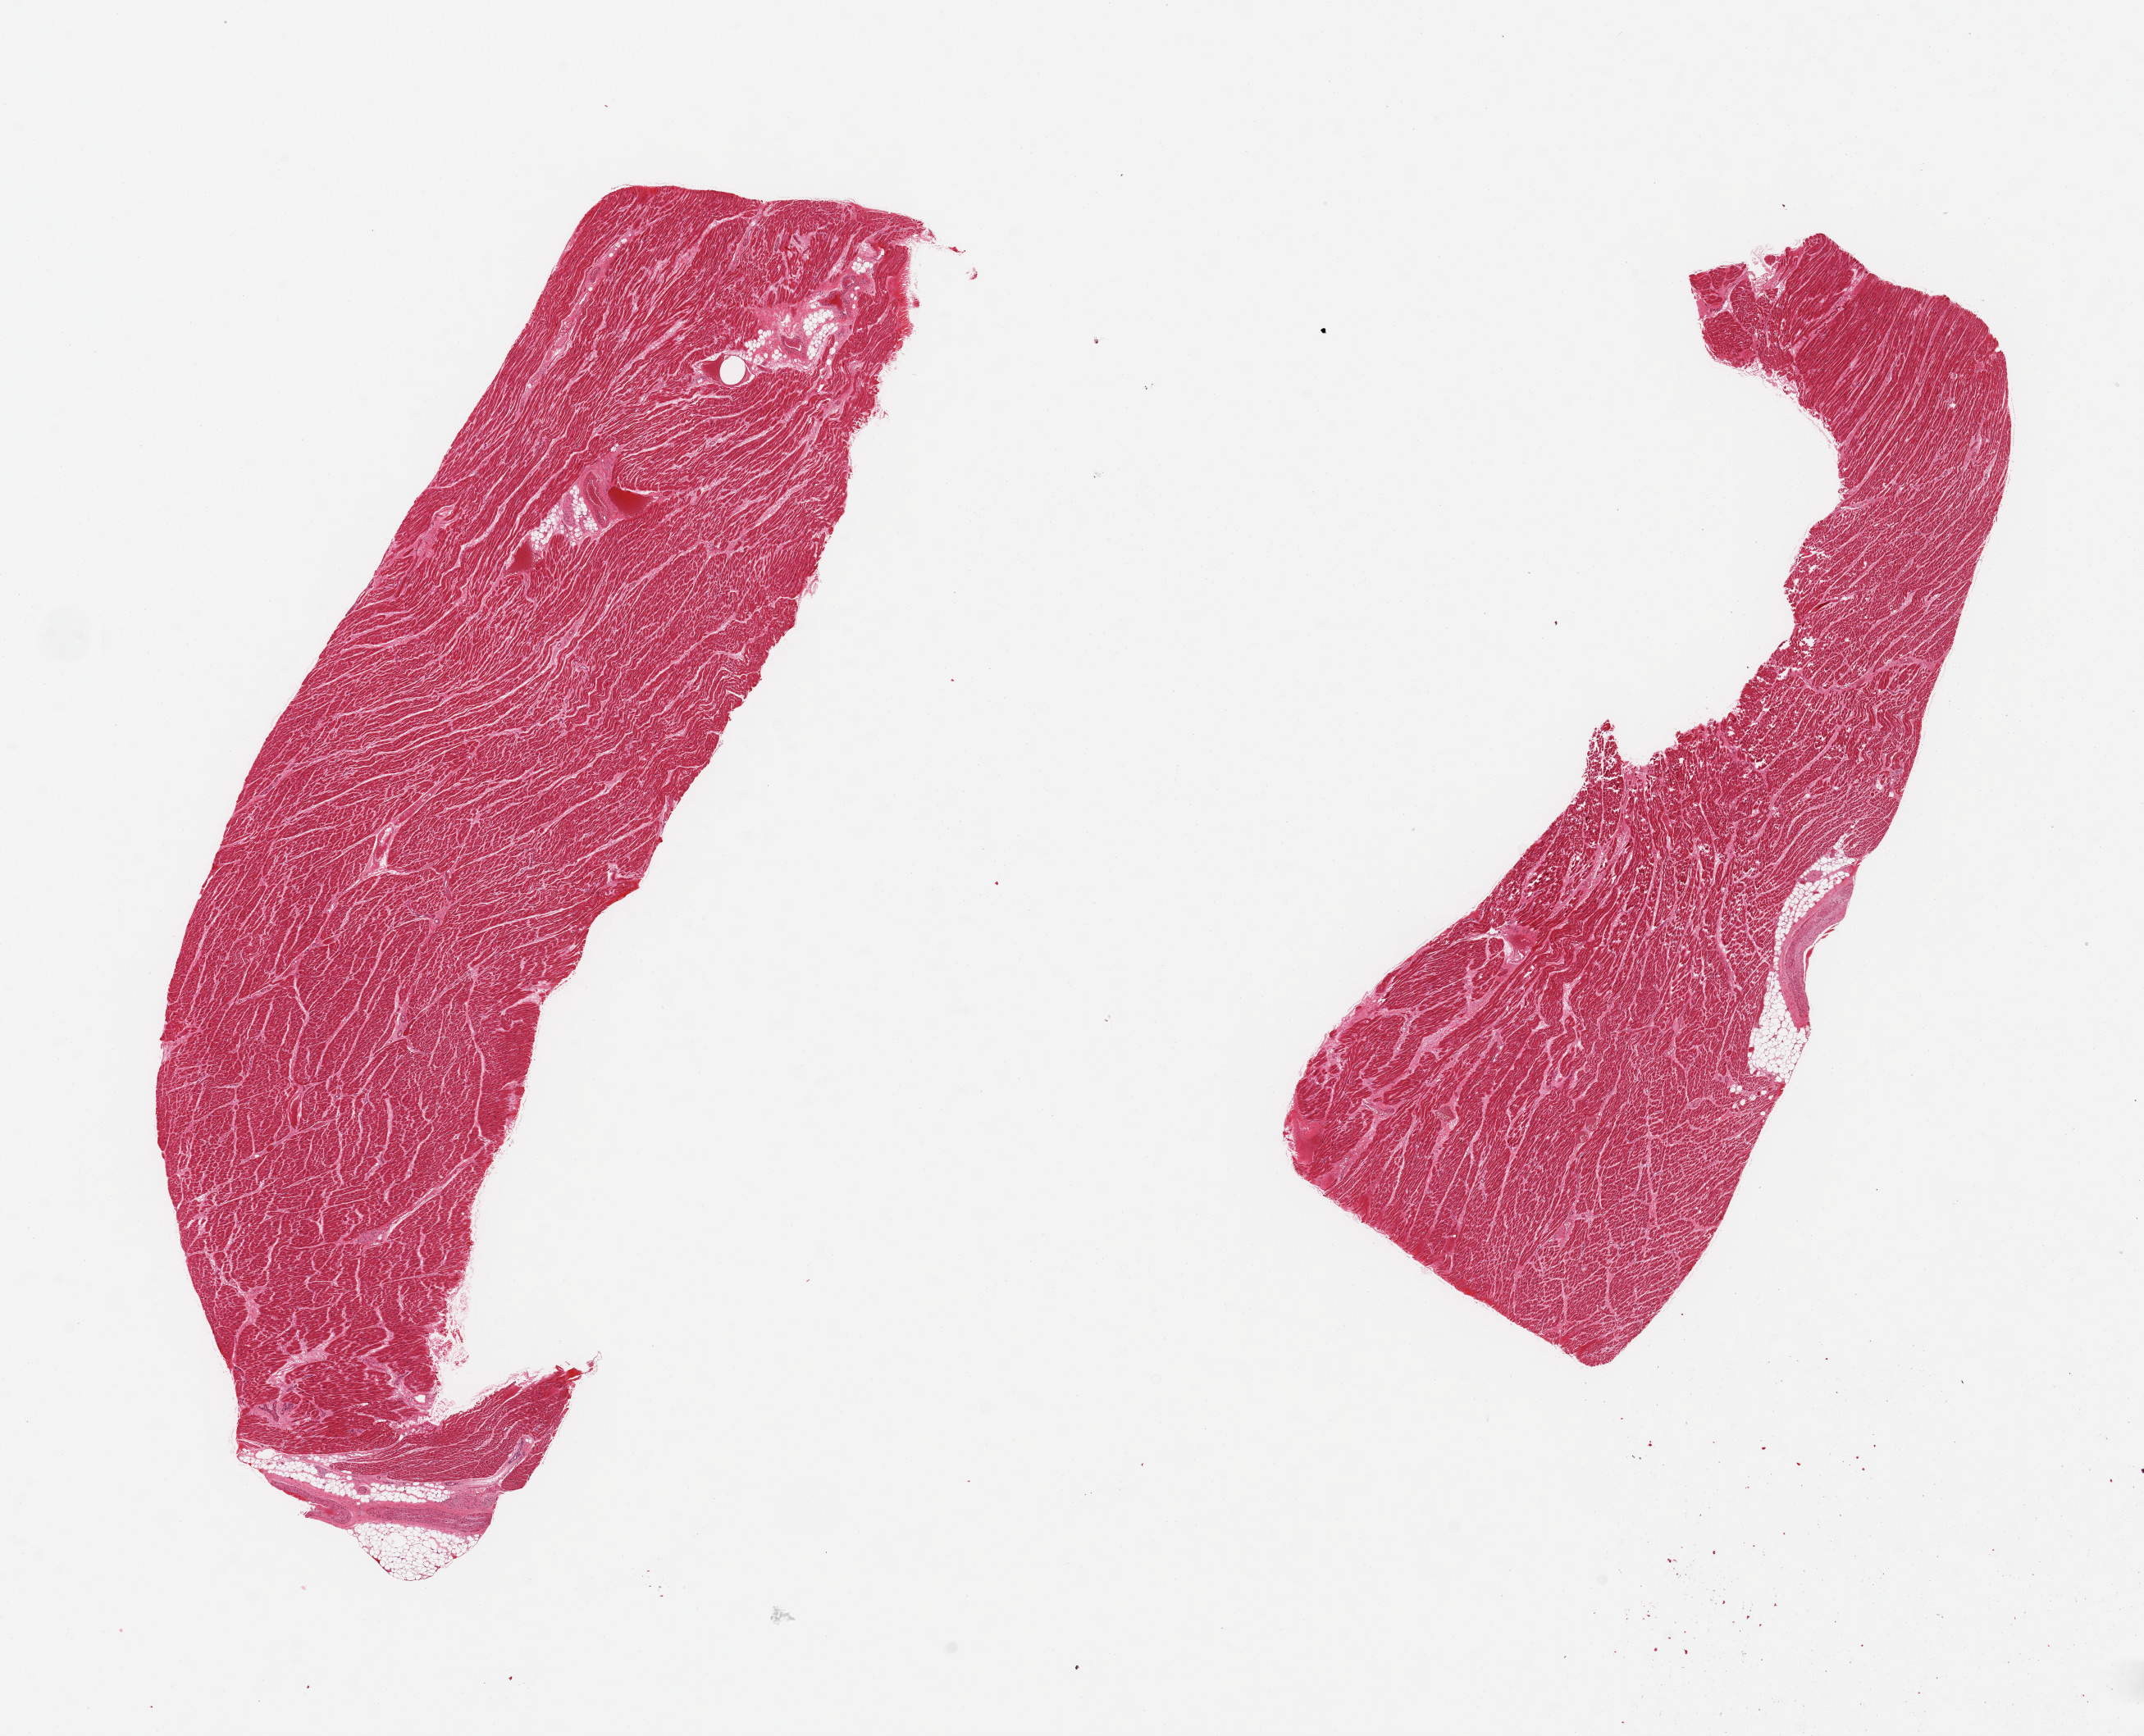
Whole-slide image, H&E stain, whole scanned area (about 20.7 x 16.7 mm, slide scanned at 20x) shown as a low-resolution overview, PAXgene-fixed, paraffin-embedded tissue, target tissue: heart, tissue donor sample. Male donor.
Review note (as recorded): 2 pieces; 5% internal fat.